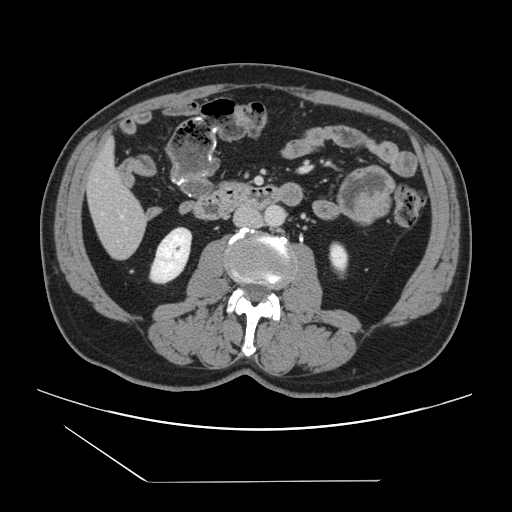
Contrast-enhanced abdominal CT, one axial slice; position 31 of 157 along the scan axis; 120 kVp; intravenous contrast given; soft-tissue window (W 400 / L 40 HU); 2.5 mm slice thickness; 512 × 512 image matrix, field of view 407 × 407 mm. Male patient, age 61 years. Case-level facts recorded for this patient, not image findings: diagnosis: colorectal cancer liver metastases, imaged before liver resection; multiple liver metastases: yes; largest metastasis: 5.5 cm; chemotherapy before resection: no.
Outlined on this slice (expert manual segmentation):
- hepatic veins: bounding box [x1, y1, x2, y2] px = [121, 216, 123, 218]
- liver: [88, 146, 147, 258]
- planned liver remnant (the part of the liver to remain after resection): [87, 145, 142, 219]